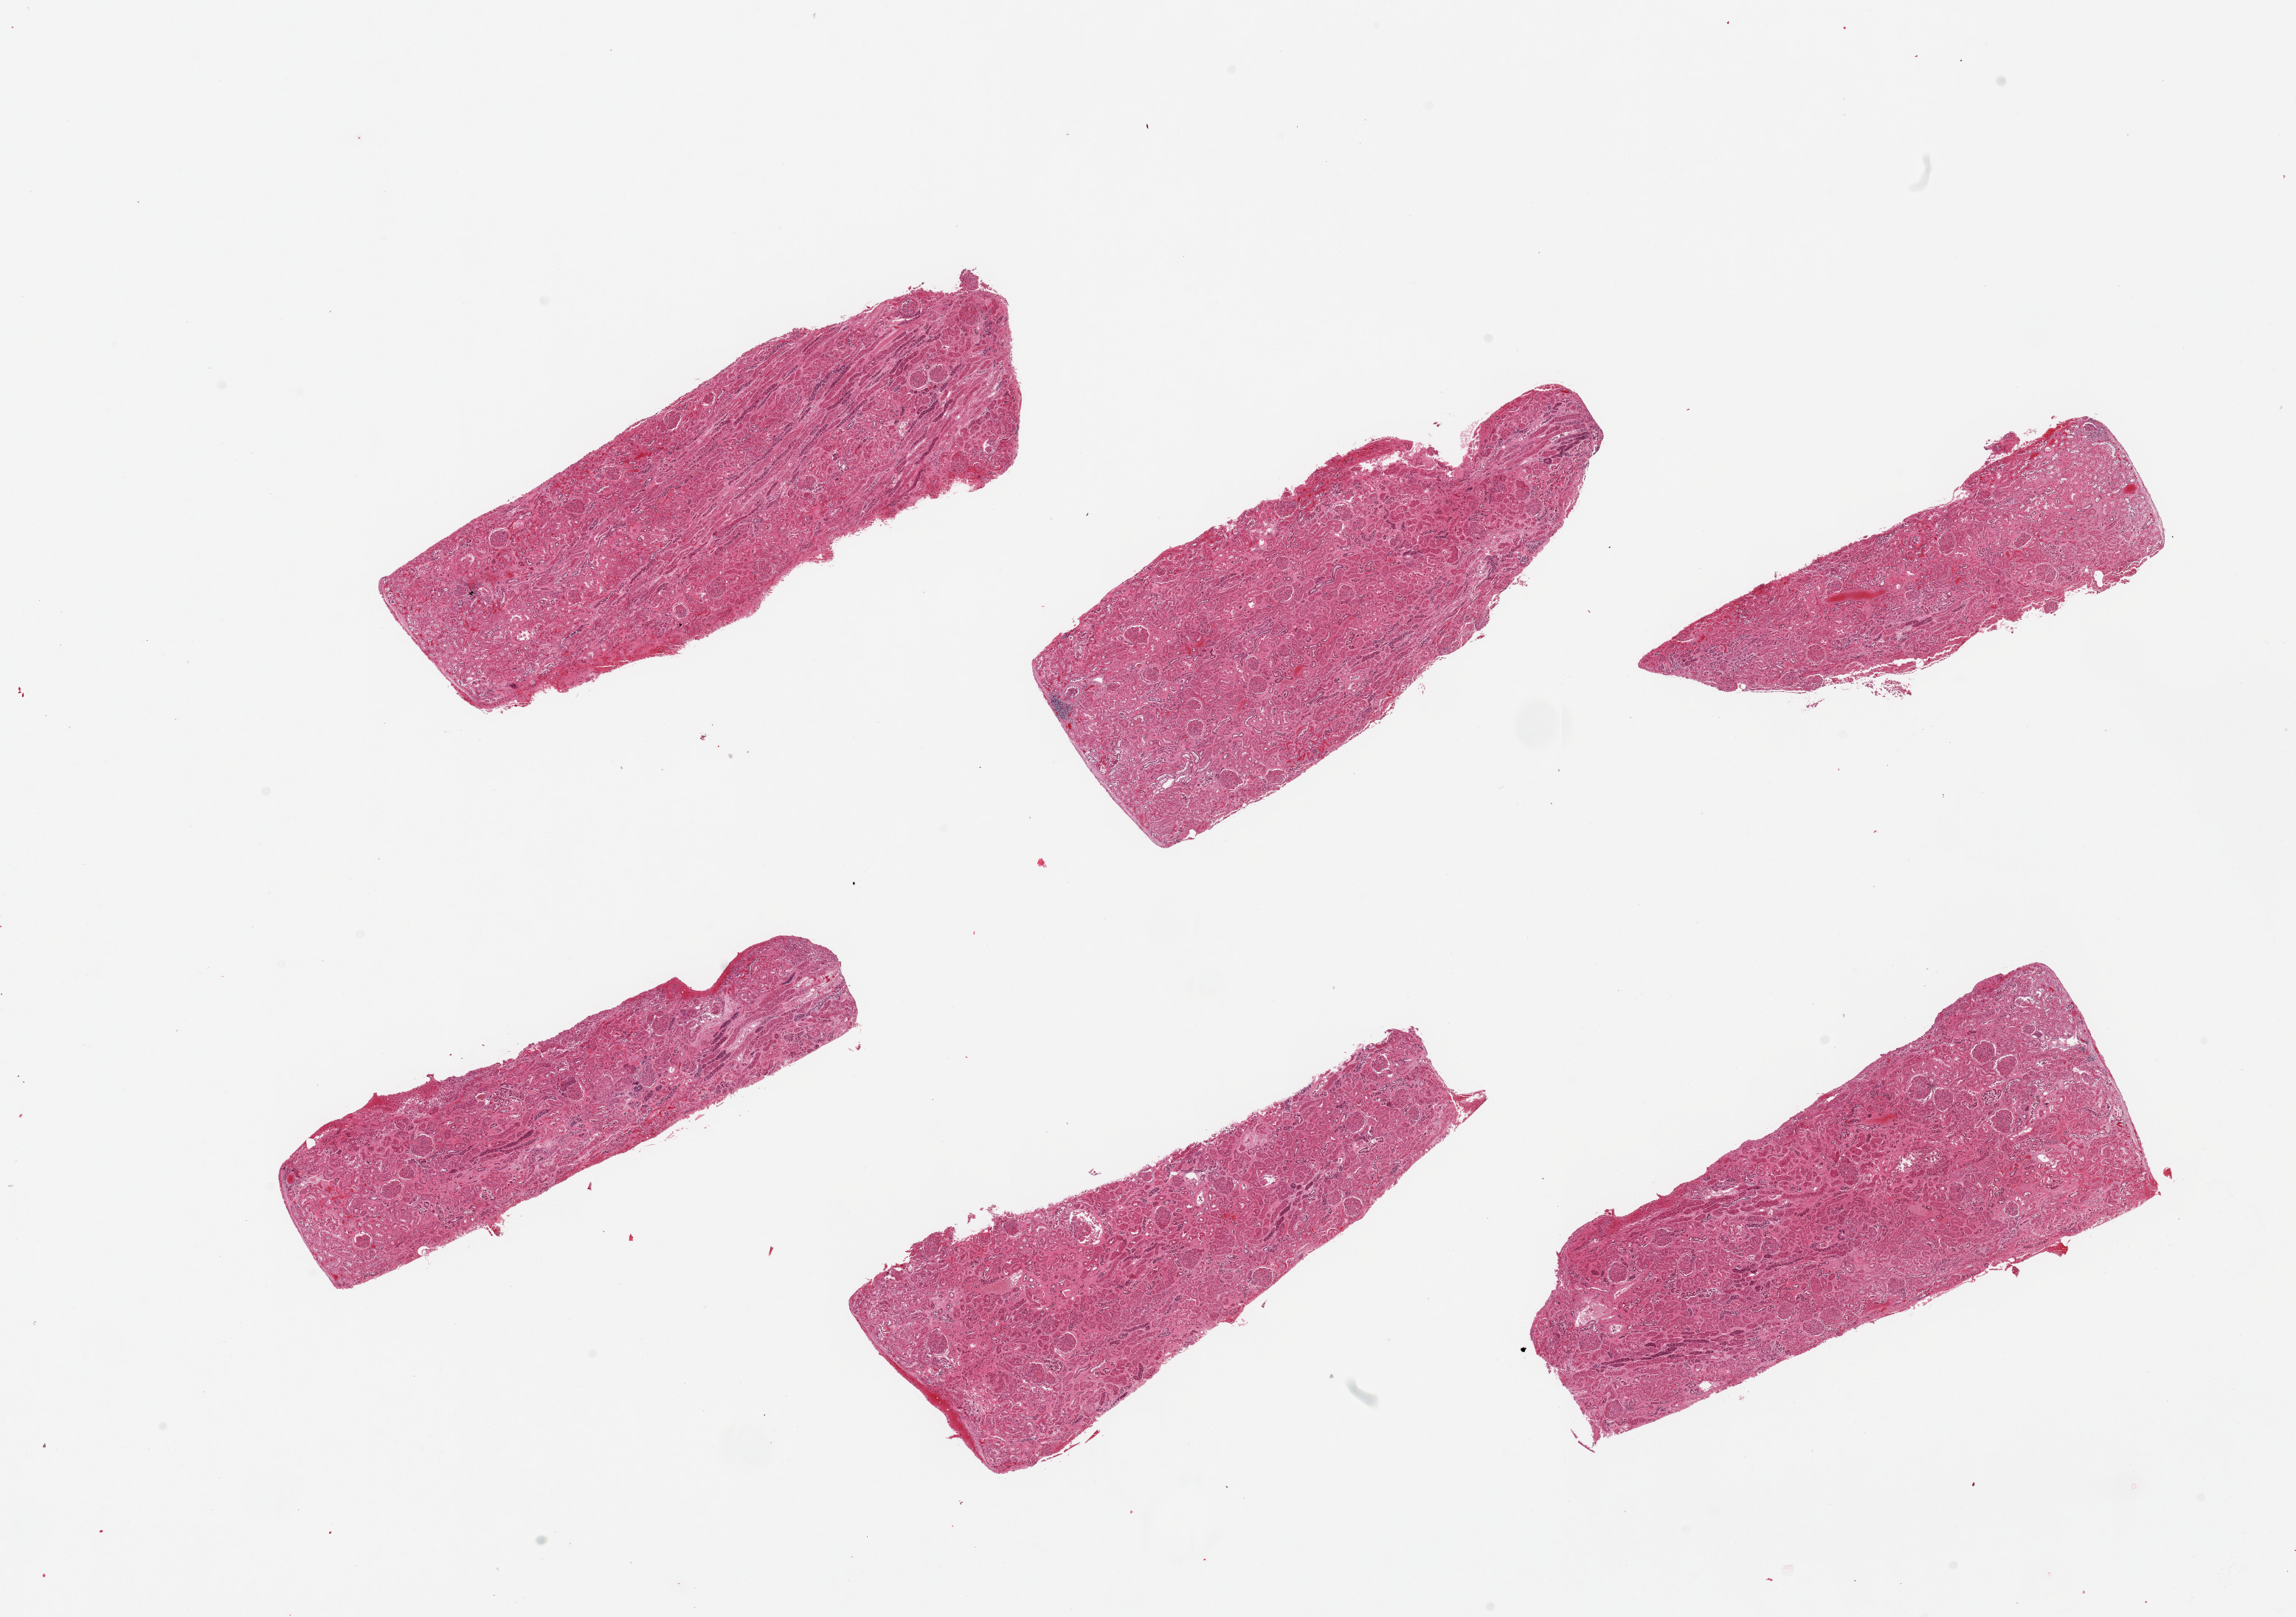
Hematoxylin and eosin (H&E) whole-slide image, shown as a low-resolution overview of the whole scanned area (about 24.6 x 17.3 mm, from a 20x scan); PAXgene-fixed paraffin-embedded (PFPE) section; section of renal cortex (target tissue); tissue donor sample.
Review note (as recorded): 6 pieces, glomeruli present, tubules with advanced autolysis.